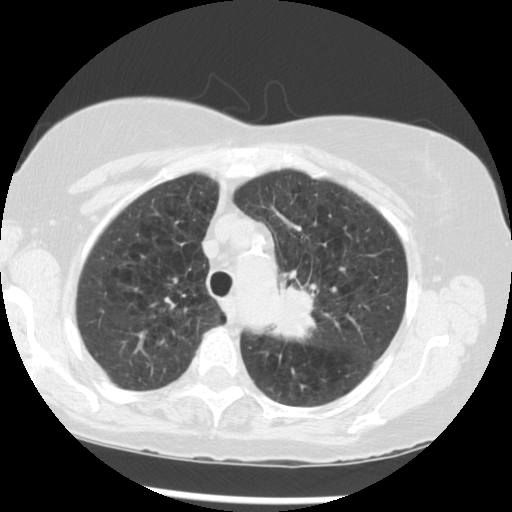
Low-dose screening chest CT, one axial slice. Slice 218 of 283 in the series (ordered by position). Lung window (W 1500 / L -600 HU). 2.5 mm slice thickness. 512 × 512 image matrix.
Annotated regions visible in this slice (manually delineated by an expert):
- lesion 1 (tumor, upper lobe of left lung): bounding box (x1, y1, x2, y2) in pixels: (272, 287, 314, 339)